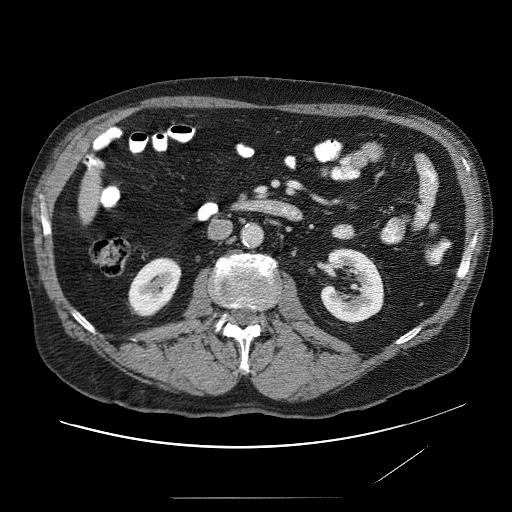
Contrast-enhanced abdominal CT (liver protocol), one axial slice. Position 6 of 89 along the scan axis. Reconstruction kernel STANDARD. 120 kVp. Soft-tissue window (W 400 / L 40 HU). 512 × 512 image matrix, field of view 420 × 420 mm. Case-level facts recorded for this patient, not image findings: diagnosis: hepatocellular carcinoma (patient treated with transarterial chemoembolisation; whether this scan precedes or follows treatment is not stated here); TNM stage (as recorded): Stage-IVA.
Structures marked on this image (semi-automatically segmented with operator editing):
- liver parenchyma outside the tumour (the mass and vessels are separate outlines, so this box may not span the whole liver): bounding box [x1, y1, x2, y2] px = [84, 152, 106, 229]